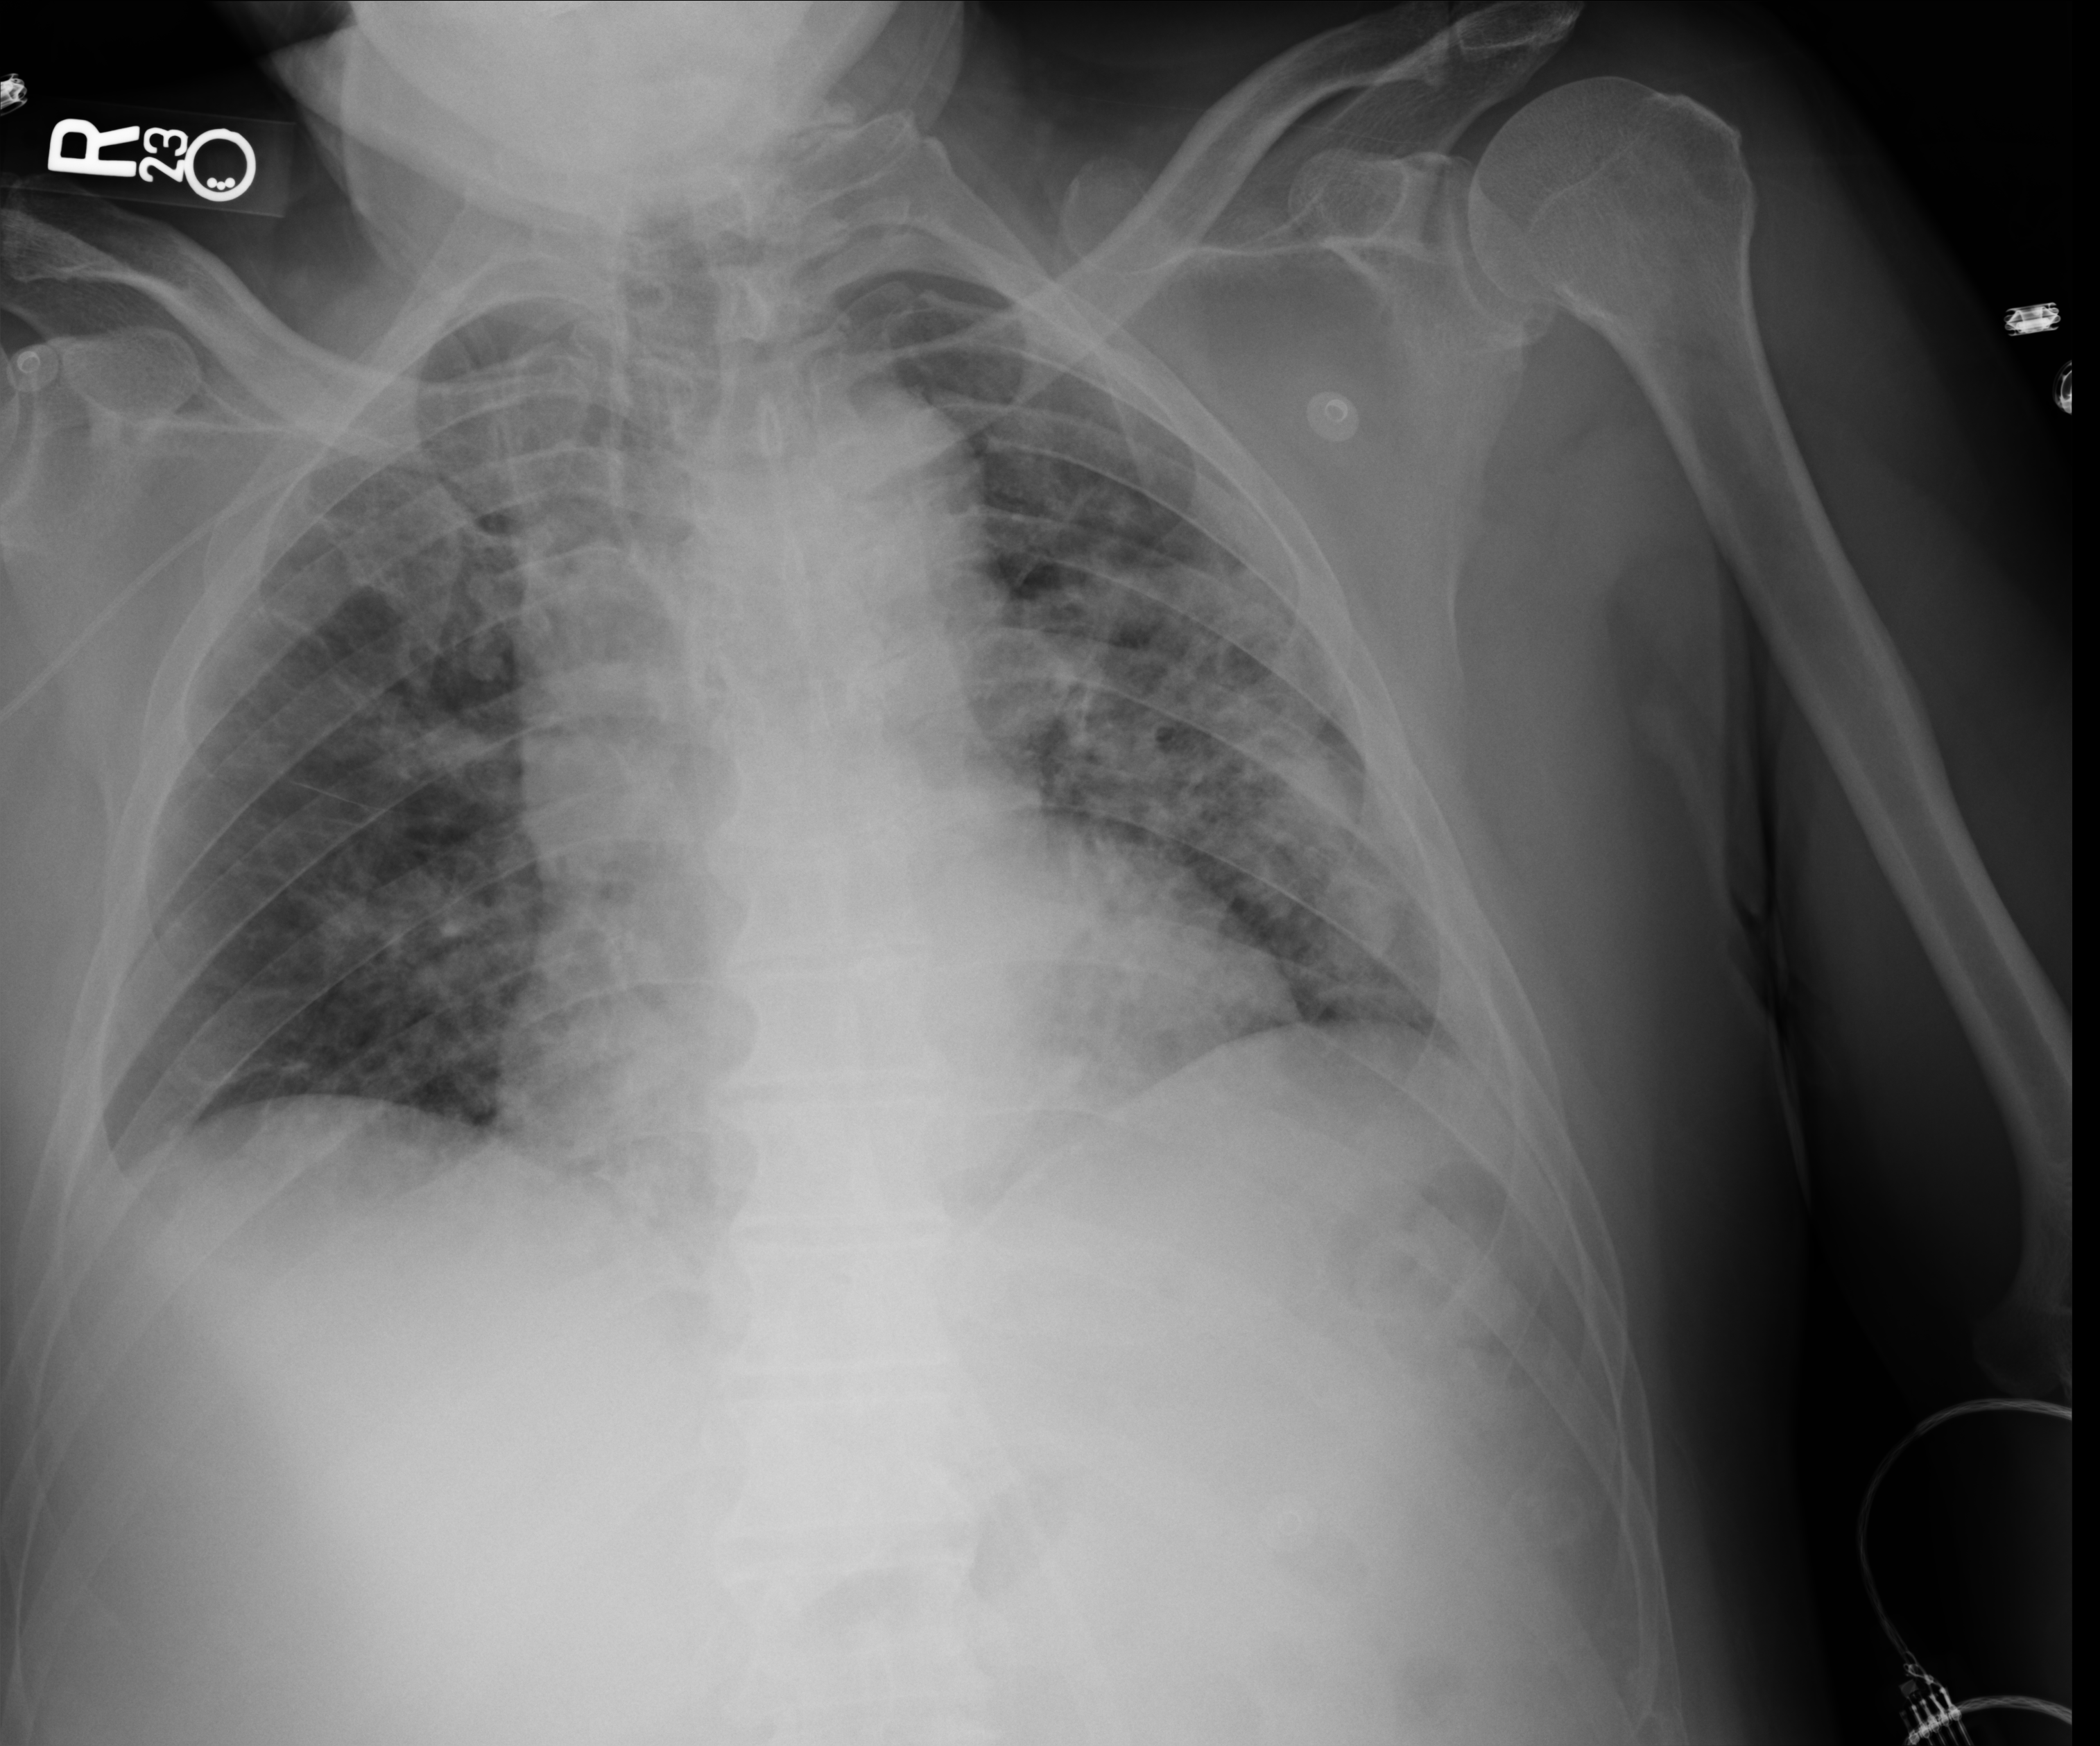
Portable chest radiograph, anteroposterior (AP) projection. Male patient hospitalised with COVID-19, age 60–74 years.
From the hospital-stay record, not from the radiograph (when in the stay this image was taken is not recorded):
- other chronic lung disease (admission record): no